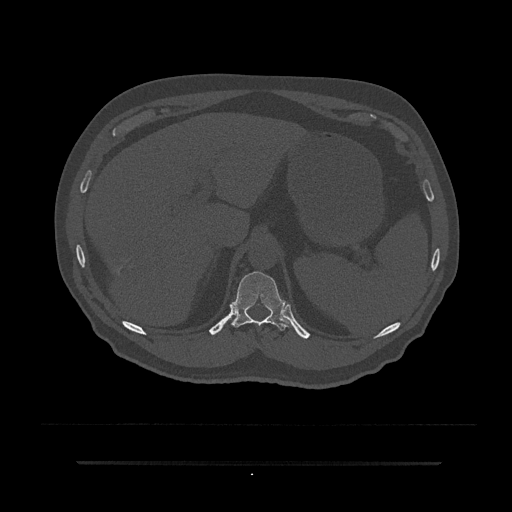
CT including the spine, one axial slice. Slice 274 of 797 in the series (ordered by position). Reconstruction kernel Br40s/3. 120 kVp. Bone window (W 1800 / L 400 HU). 0.5 mm slice thickness. 512 × 512 image matrix, field of view 464 × 464 mm. Male patient, age 59 years. From the clinical record (not read from this slice): primary cancer: bile ducts.
Structures marked on this image (semi-automatic segmentation, software-assisted and operator-edited):
- T11 vertebra: bounding box (x1, y1, x2, y2) in pixels: (231, 271, 292, 331)